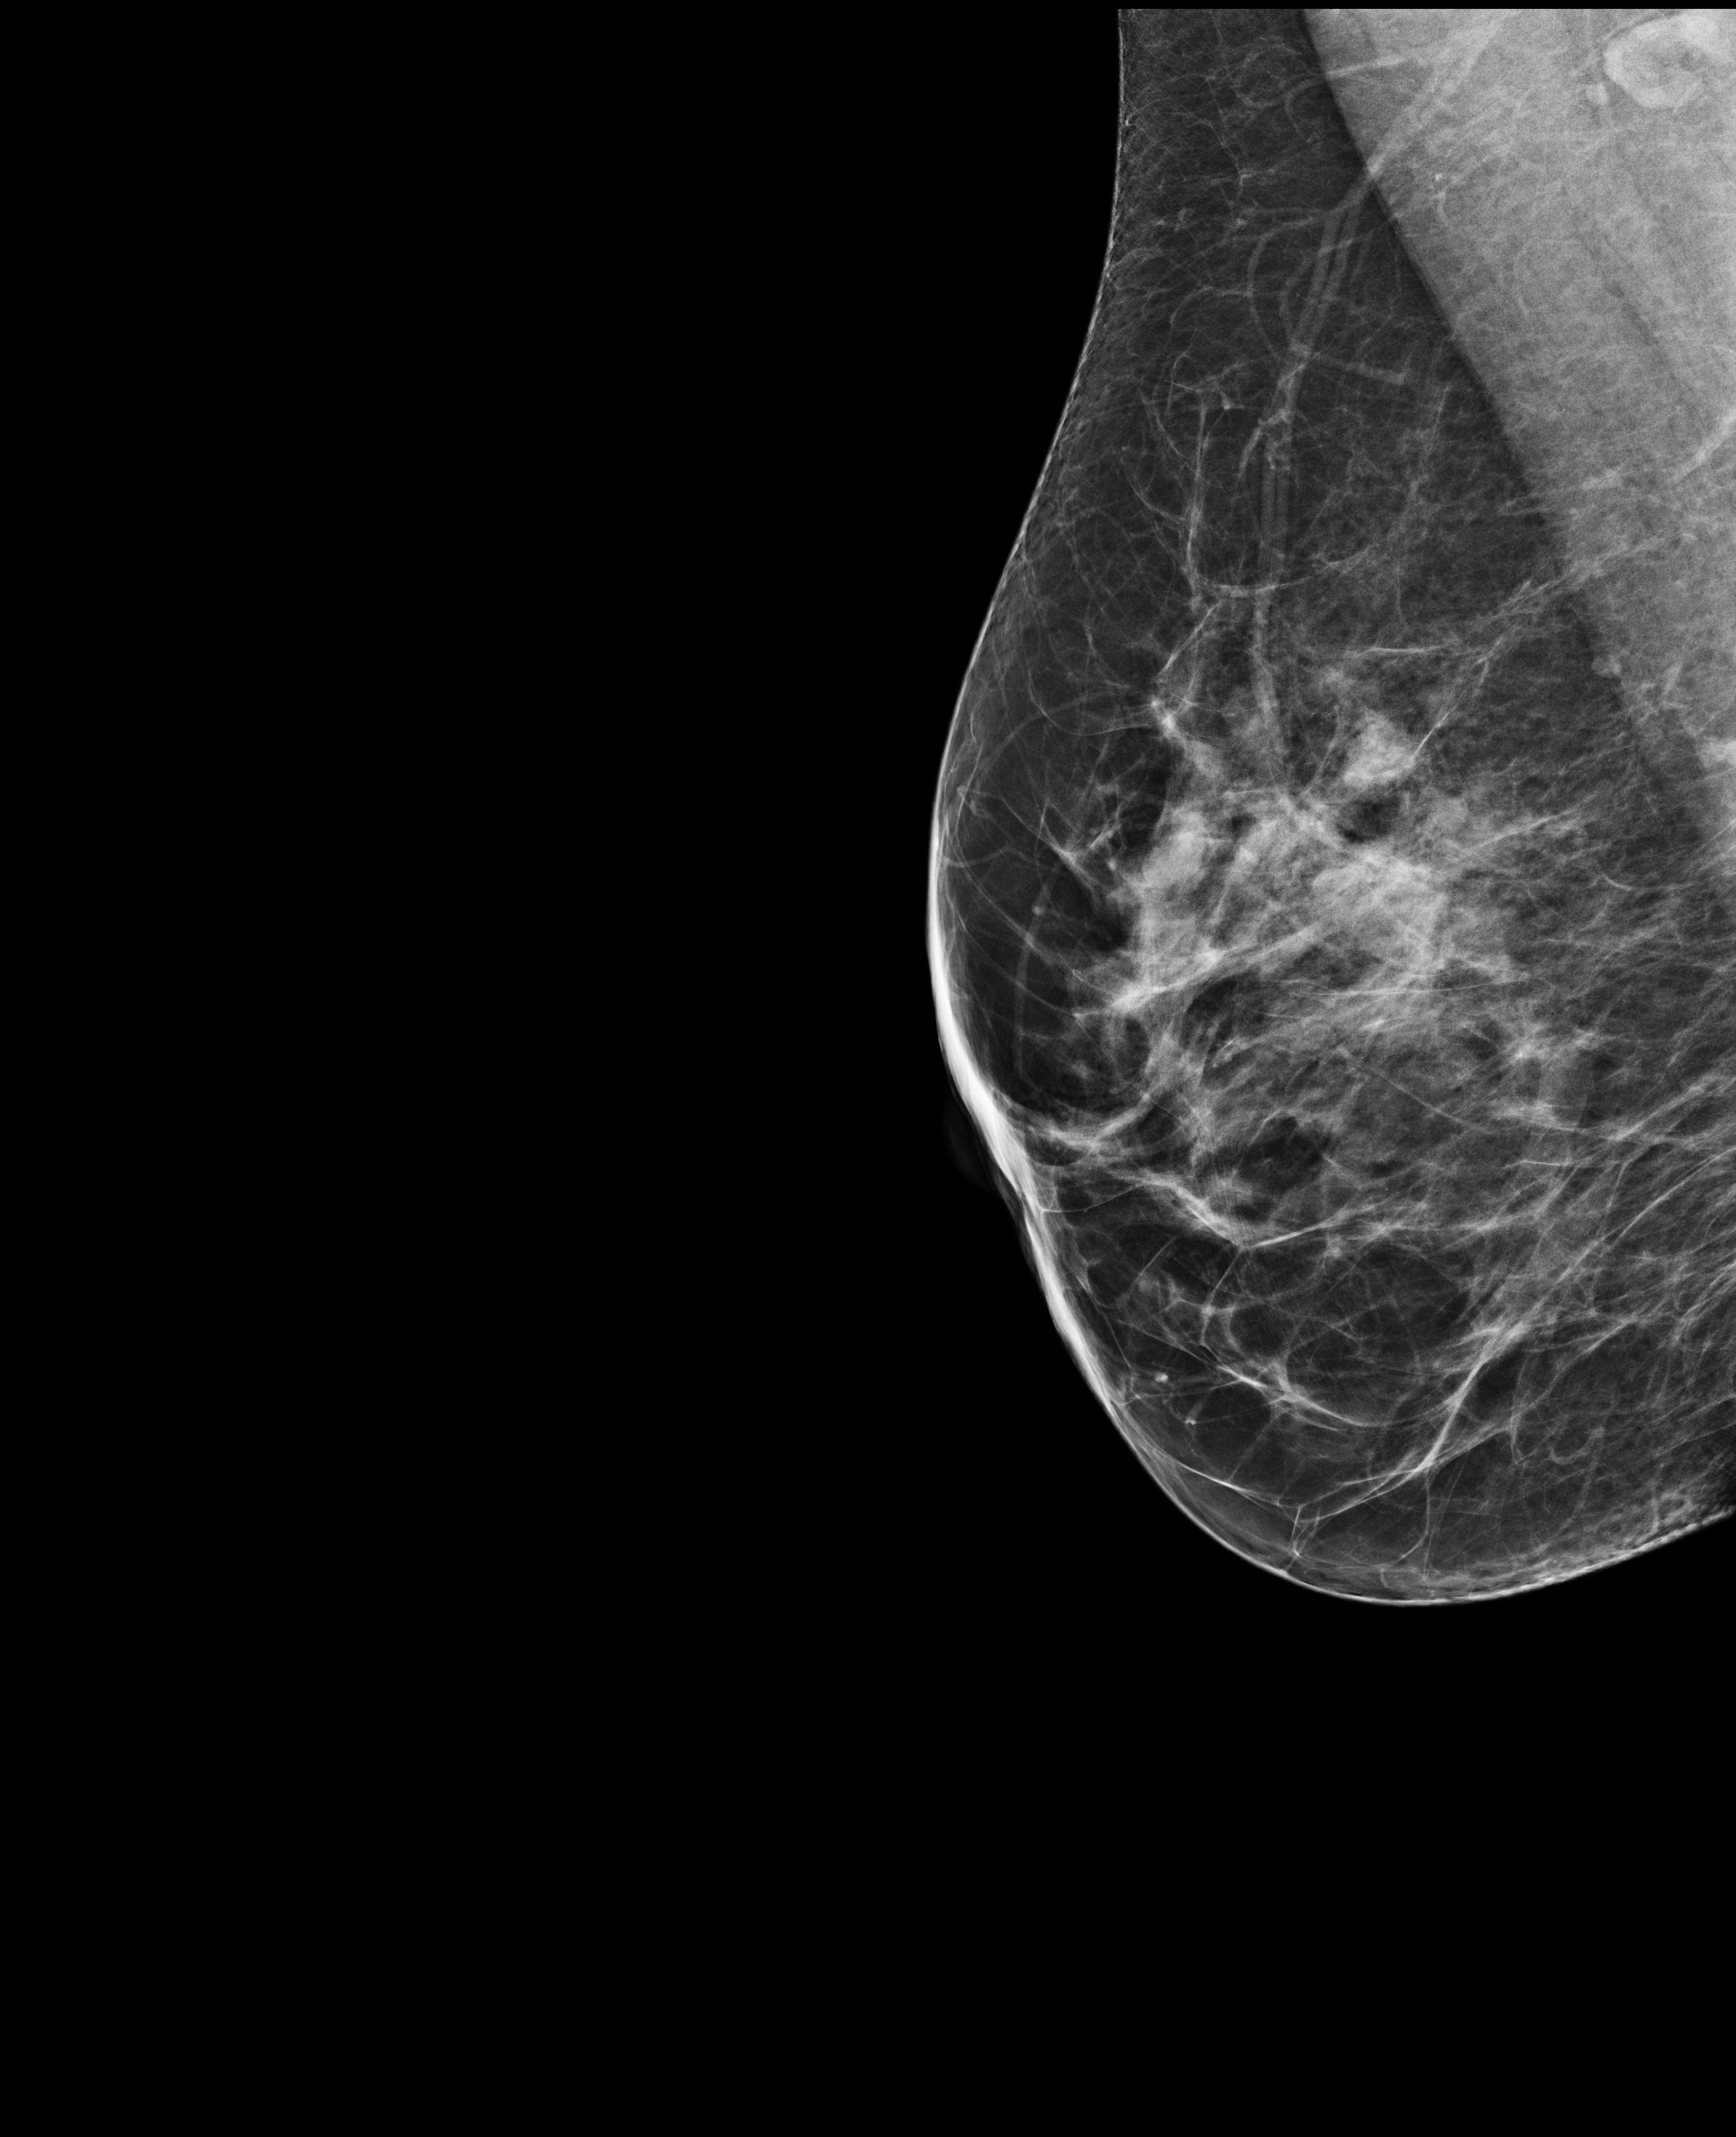
Full-field digital mammogram (FFDM); right breast; medio-lateral oblique projection; screening examination; compressed breast thickness 65 mm. Female patient, age 44 years.
BI-RADS breast density category at the screening exam (both breasts, scale 1–4): 3.